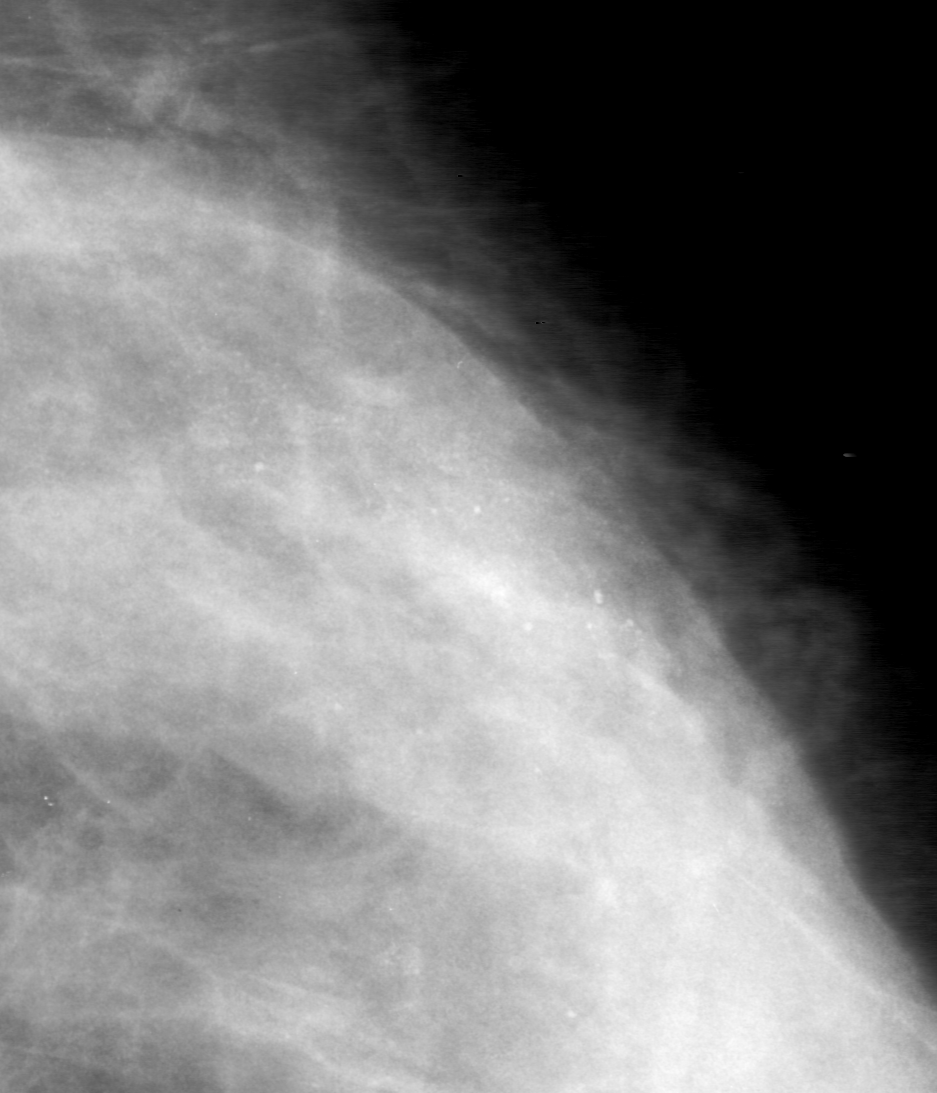
Crop from a digitized film mammogram around one marked abnormality; left breast; CC view; BI-RADS breast density category 3 (scale 1–4).
Calcifications, morphology amorphous, distribution segmental; BI-RADS assessment category 0 (incomplete: needs additional imaging); pathology result (as recorded, not read from the image): benign.